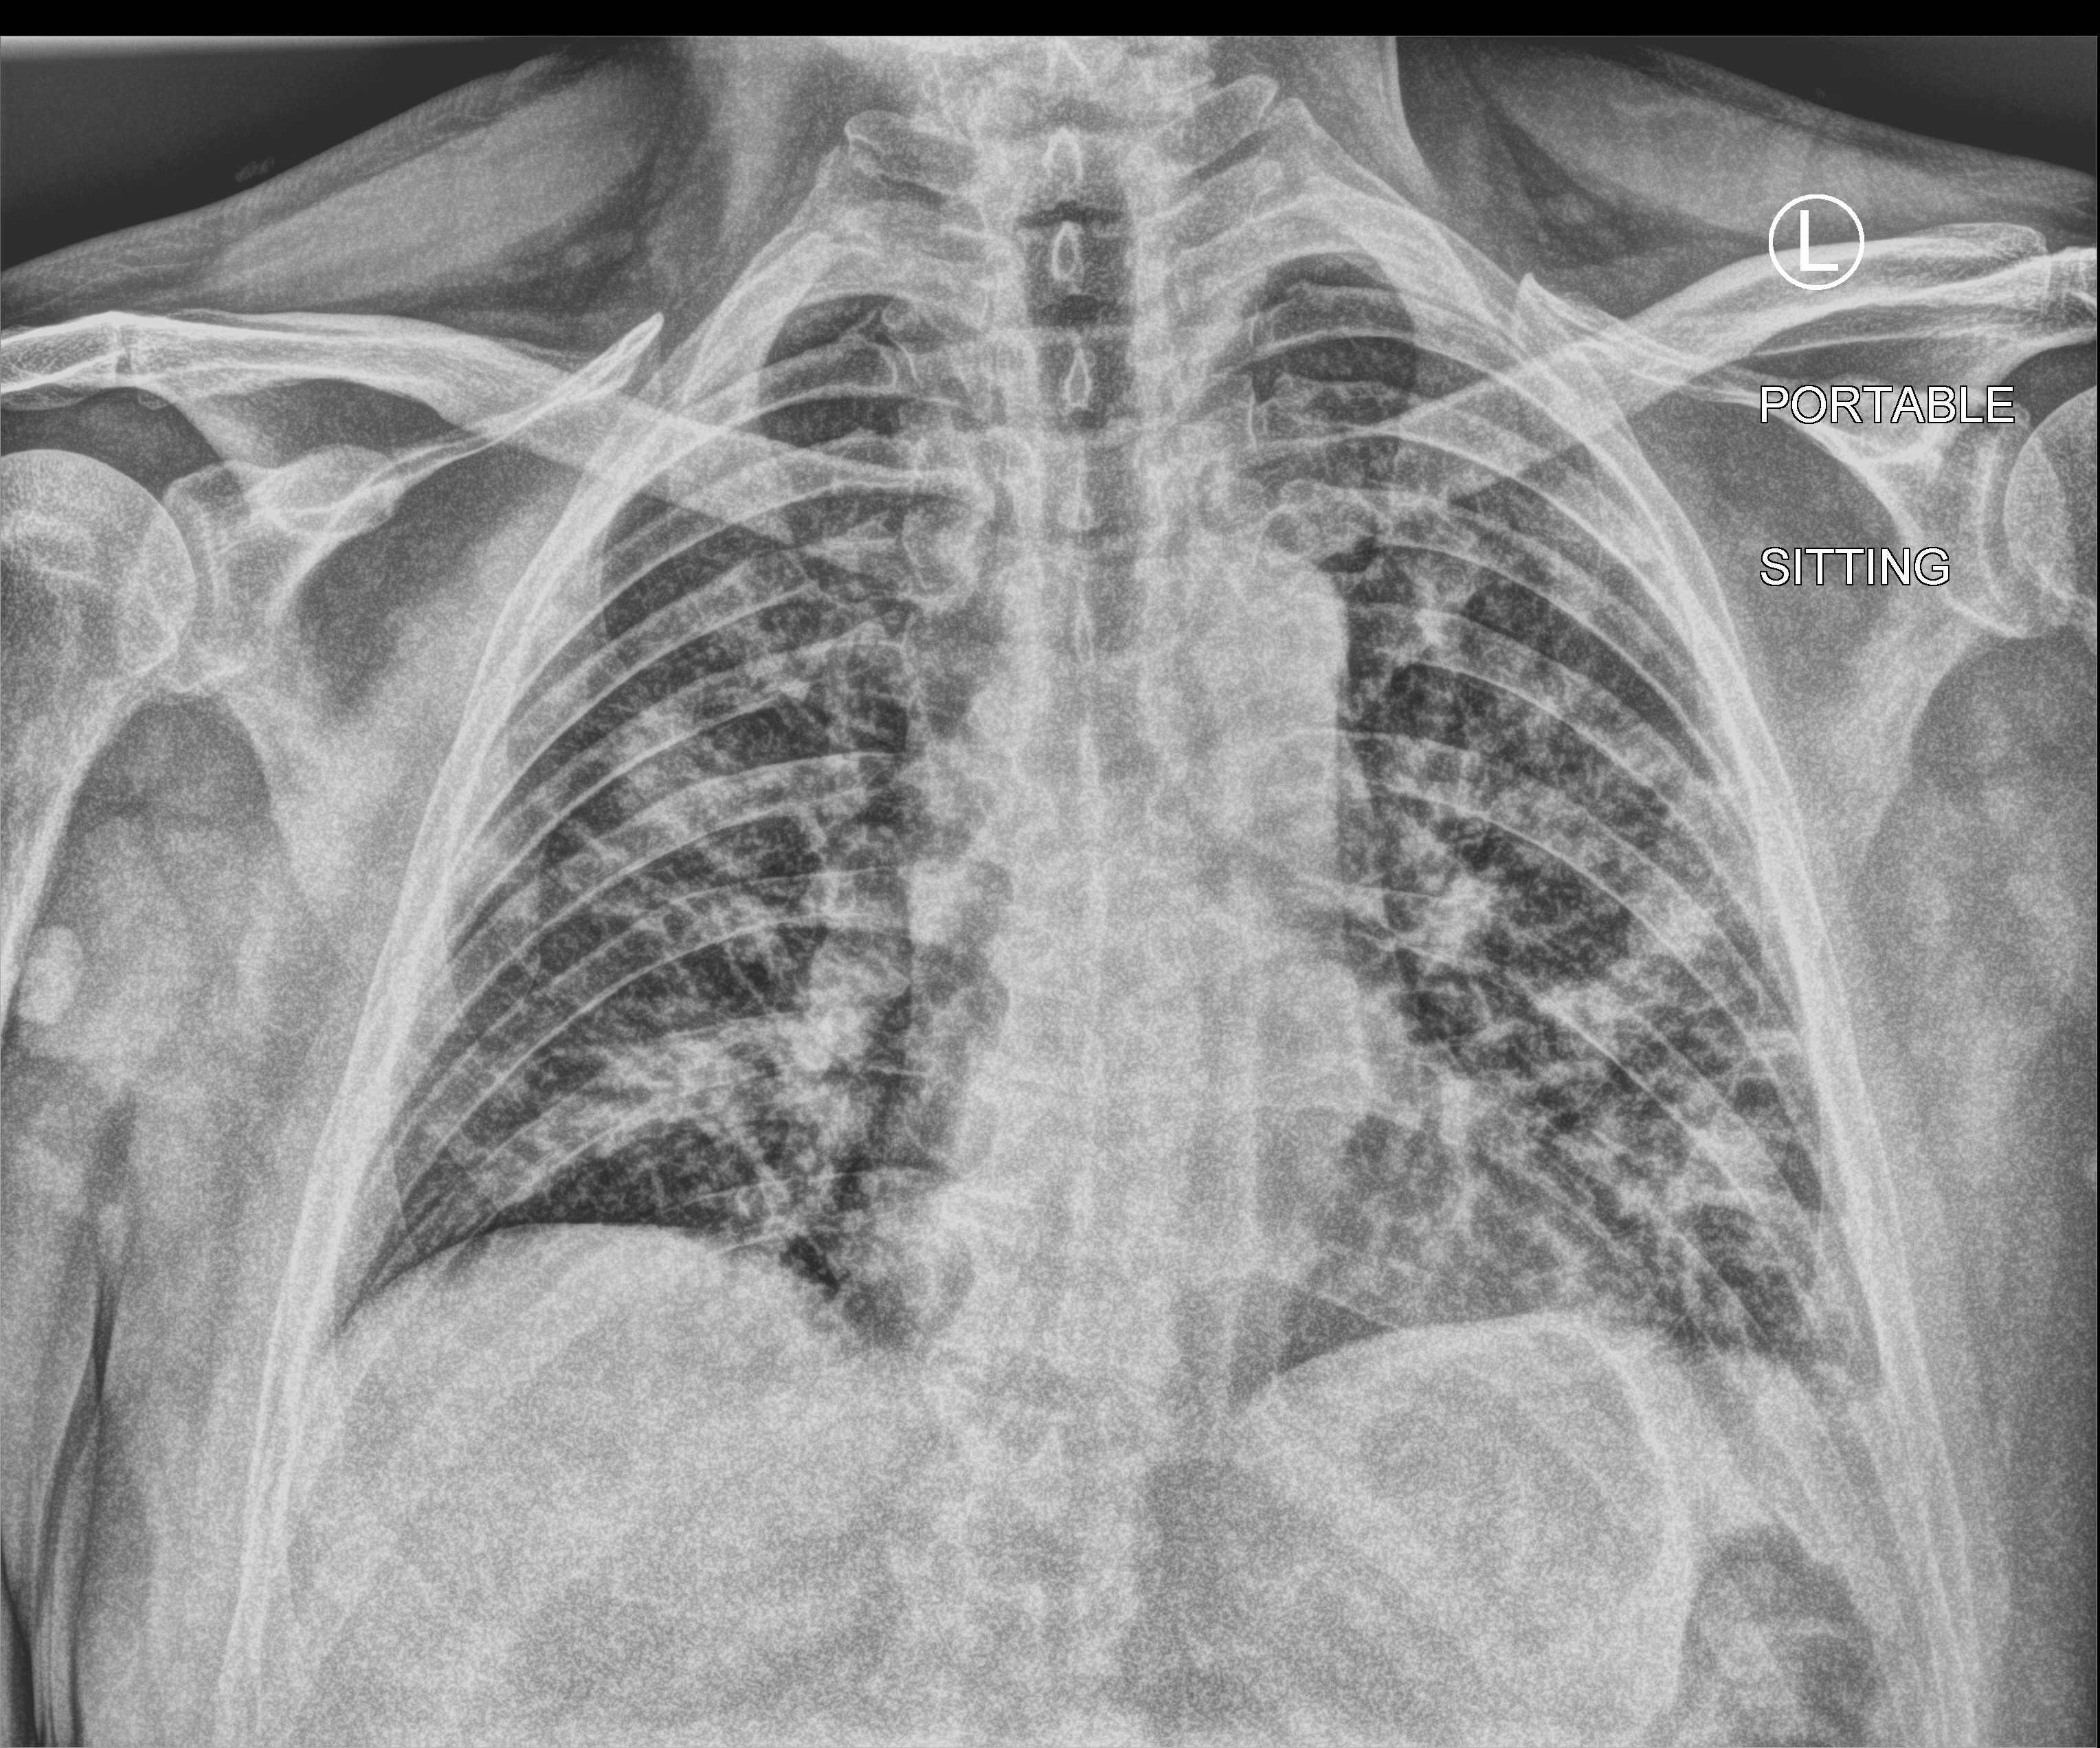
Chest X-ray (portable), anteroposterior (AP) projection. Patient hospitalised with COVID-19; male, aged 18–59 years.
Admission-level facts for this patient (not findings on this image; timing relative to this image not recorded):
- COPD (admission record): no
- admitted to intensive care during this hospital stay: no
- hypertension (admission record): no